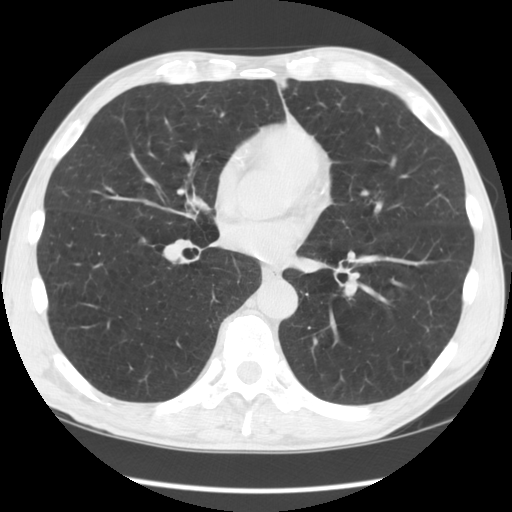
Low-dose screening chest CT, one axial slice; position 54 of 135 along the scan axis; 120 kVp; lung window (W 1500 / L -600 HU); 512 × 512 image matrix.
Structures marked on this image (manually delineated by an expert):
- lesion 1 (tumor, lower lobe of right lung): box from (x=143, y=238) to (x=145, y=242) px